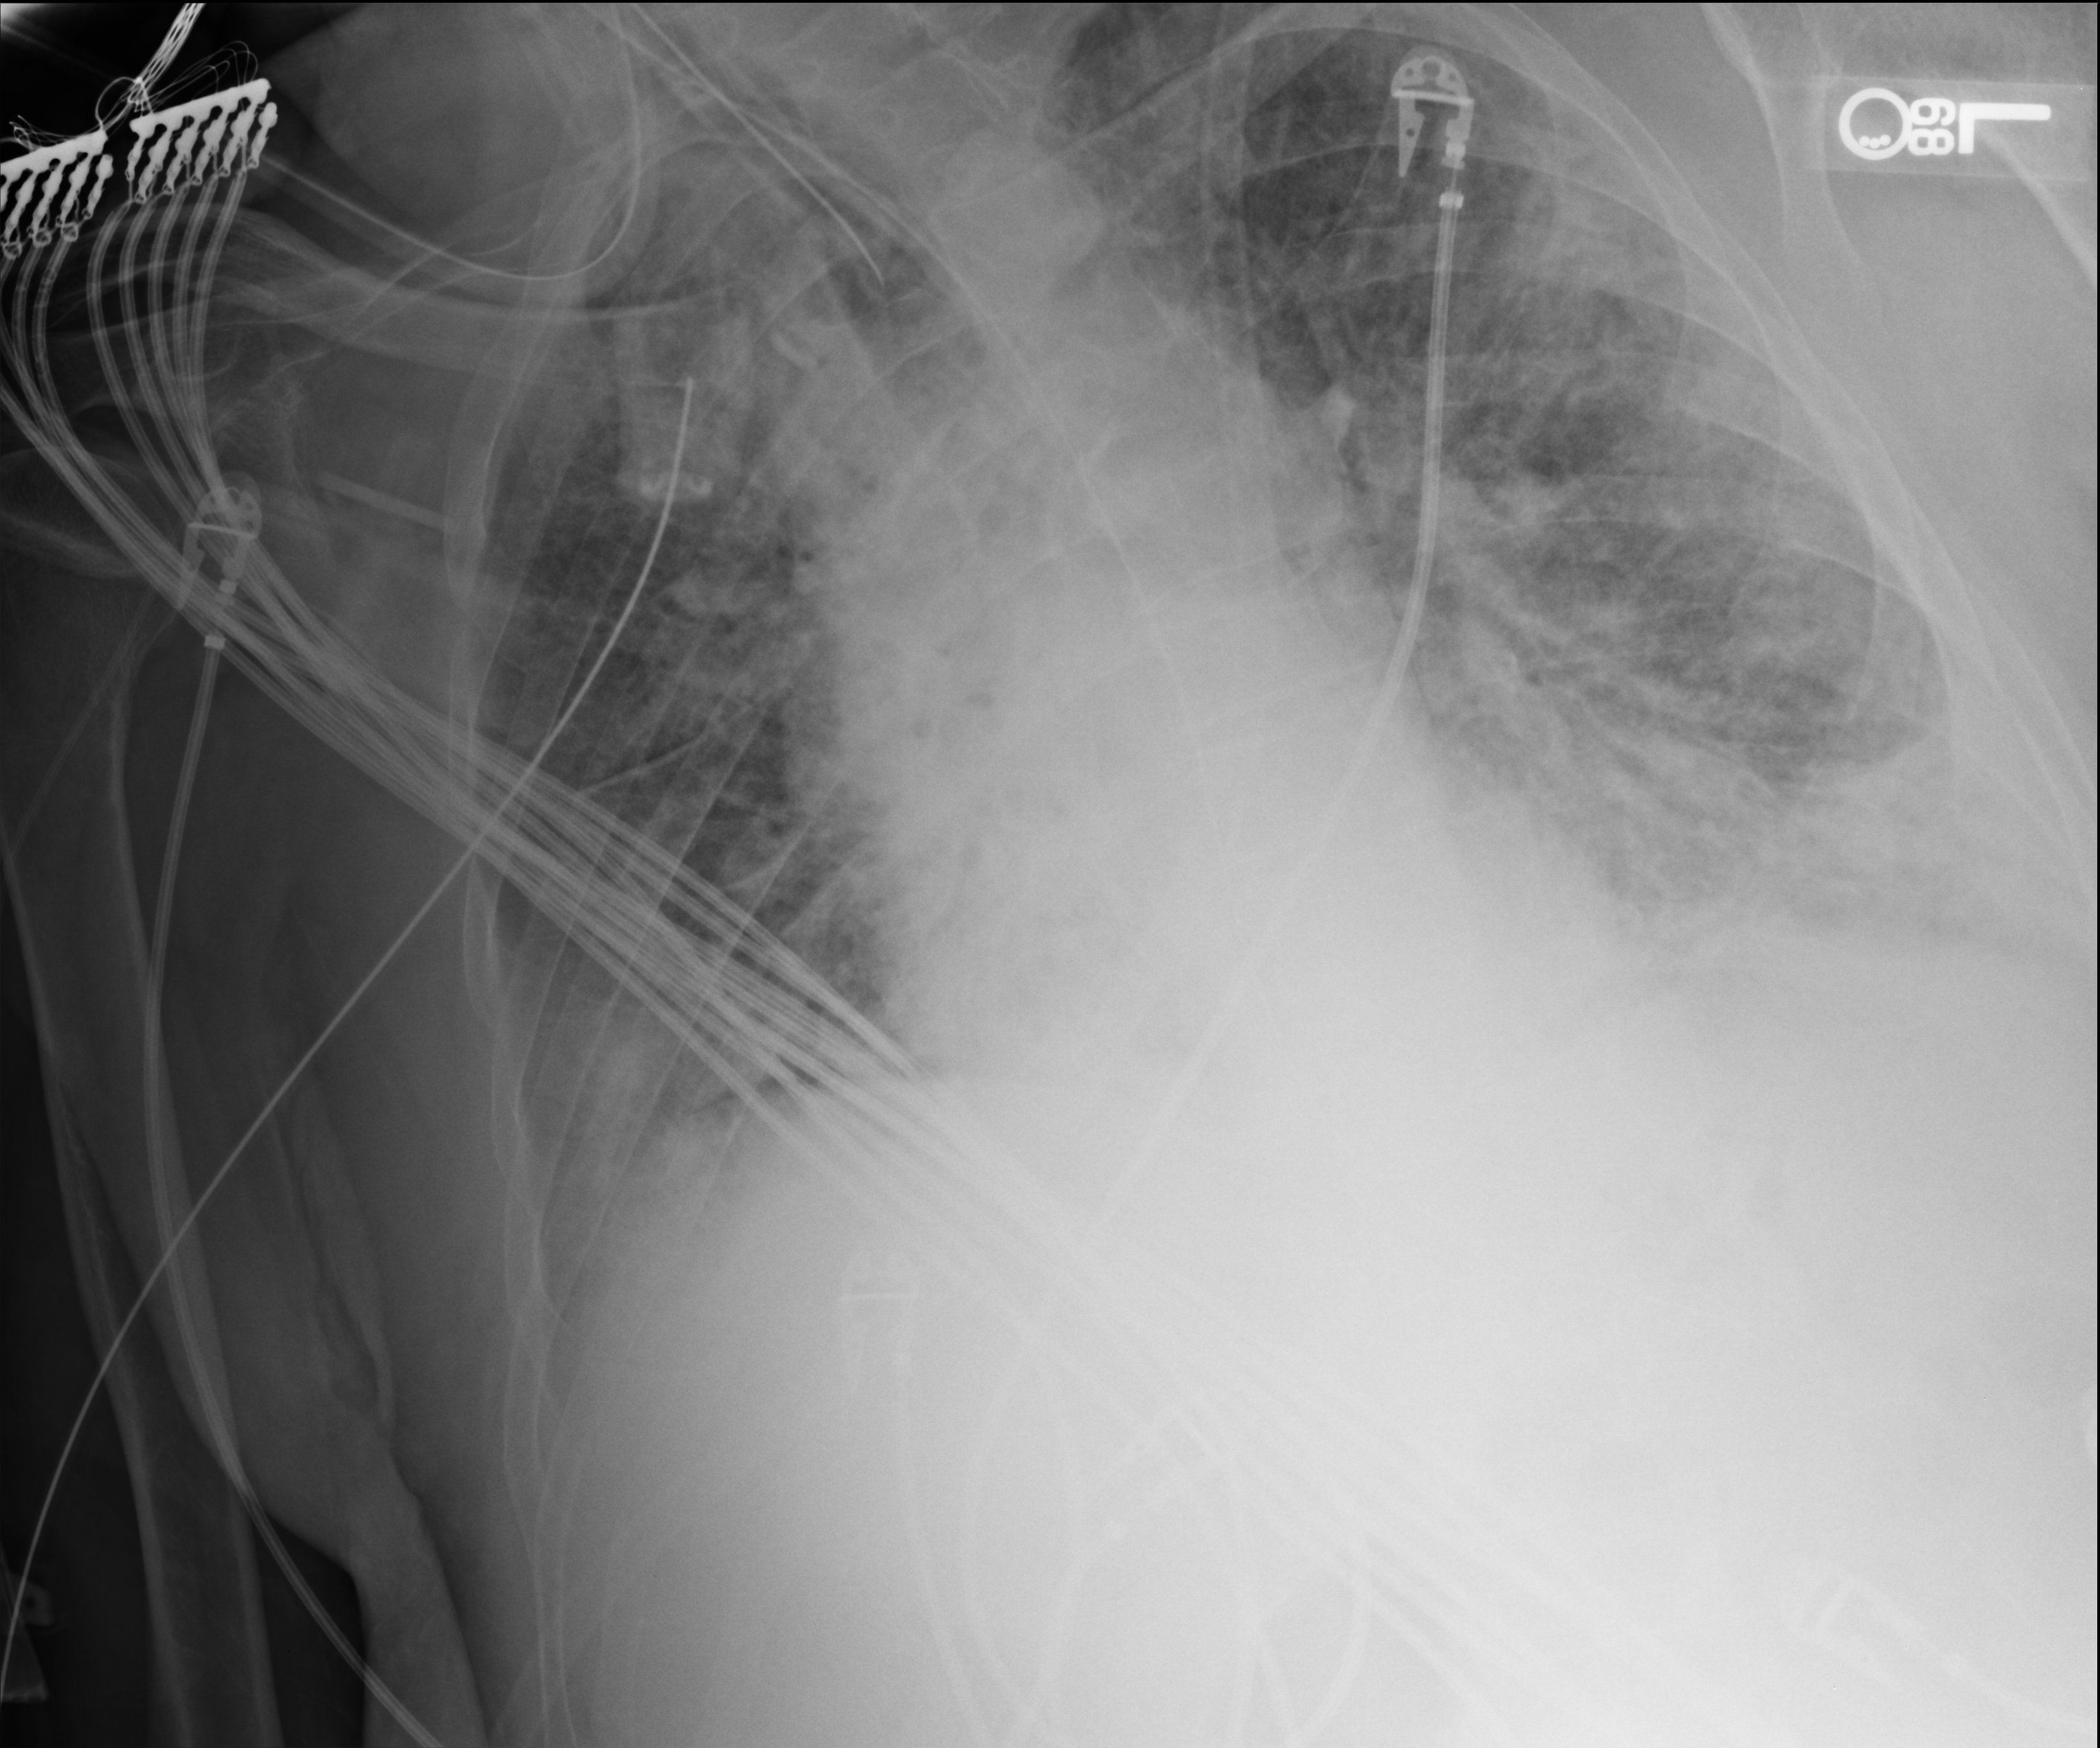
Bedside chest radiograph (computed radiography). Patient hospitalised with COVID-19; male, aged 60–74 years.
Admission-level facts for this patient (not findings on this image; timing relative to this image not recorded):
- mechanically ventilated during this hospital stay: yes
- admitted to intensive care during this hospital stay: yes